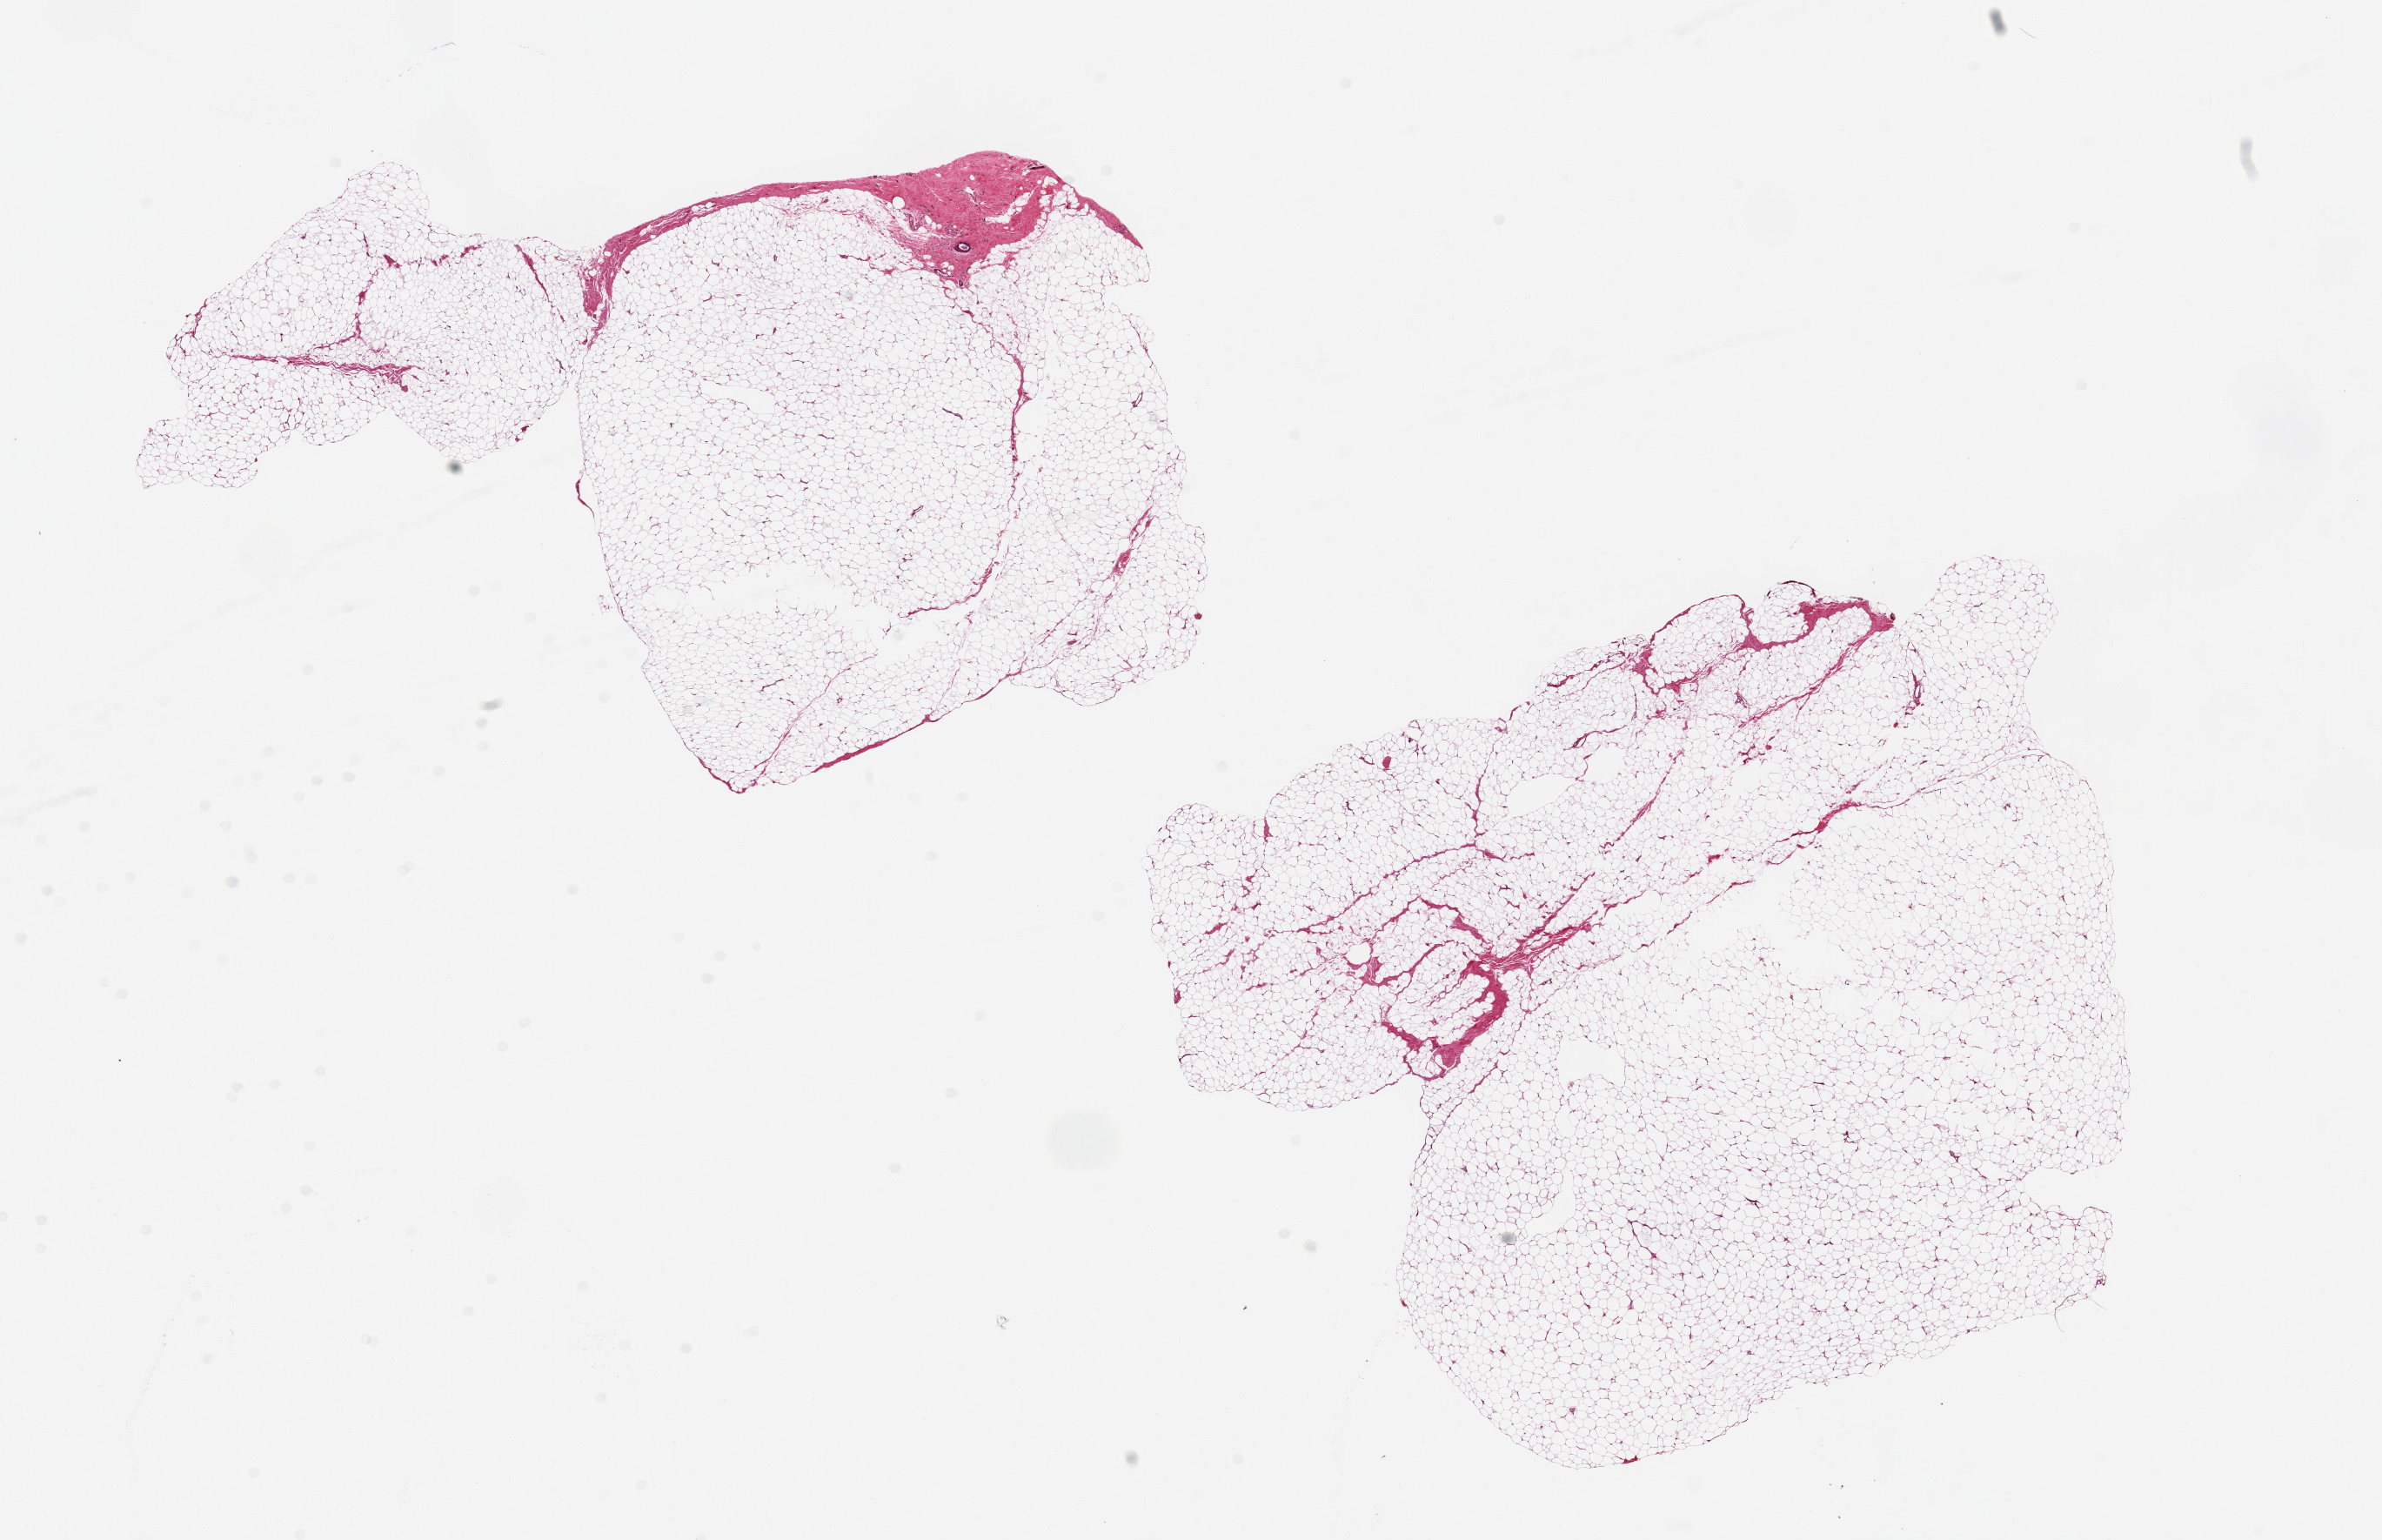
Digitized haematoxylin and eosin-stained section, a low-resolution overview of the entire scanned area, about 21.7 x 14.0 mm (slide scanned at 20x). PAXgene-fixed paraffin-embedded (PFPE) section. Section of breast (target tissue). Tissue donor sample.
* reviewer comment on this tissue sample: 2 aliquots, ~7x7mm. Single minute ductal unit noted, ~100 microns in d